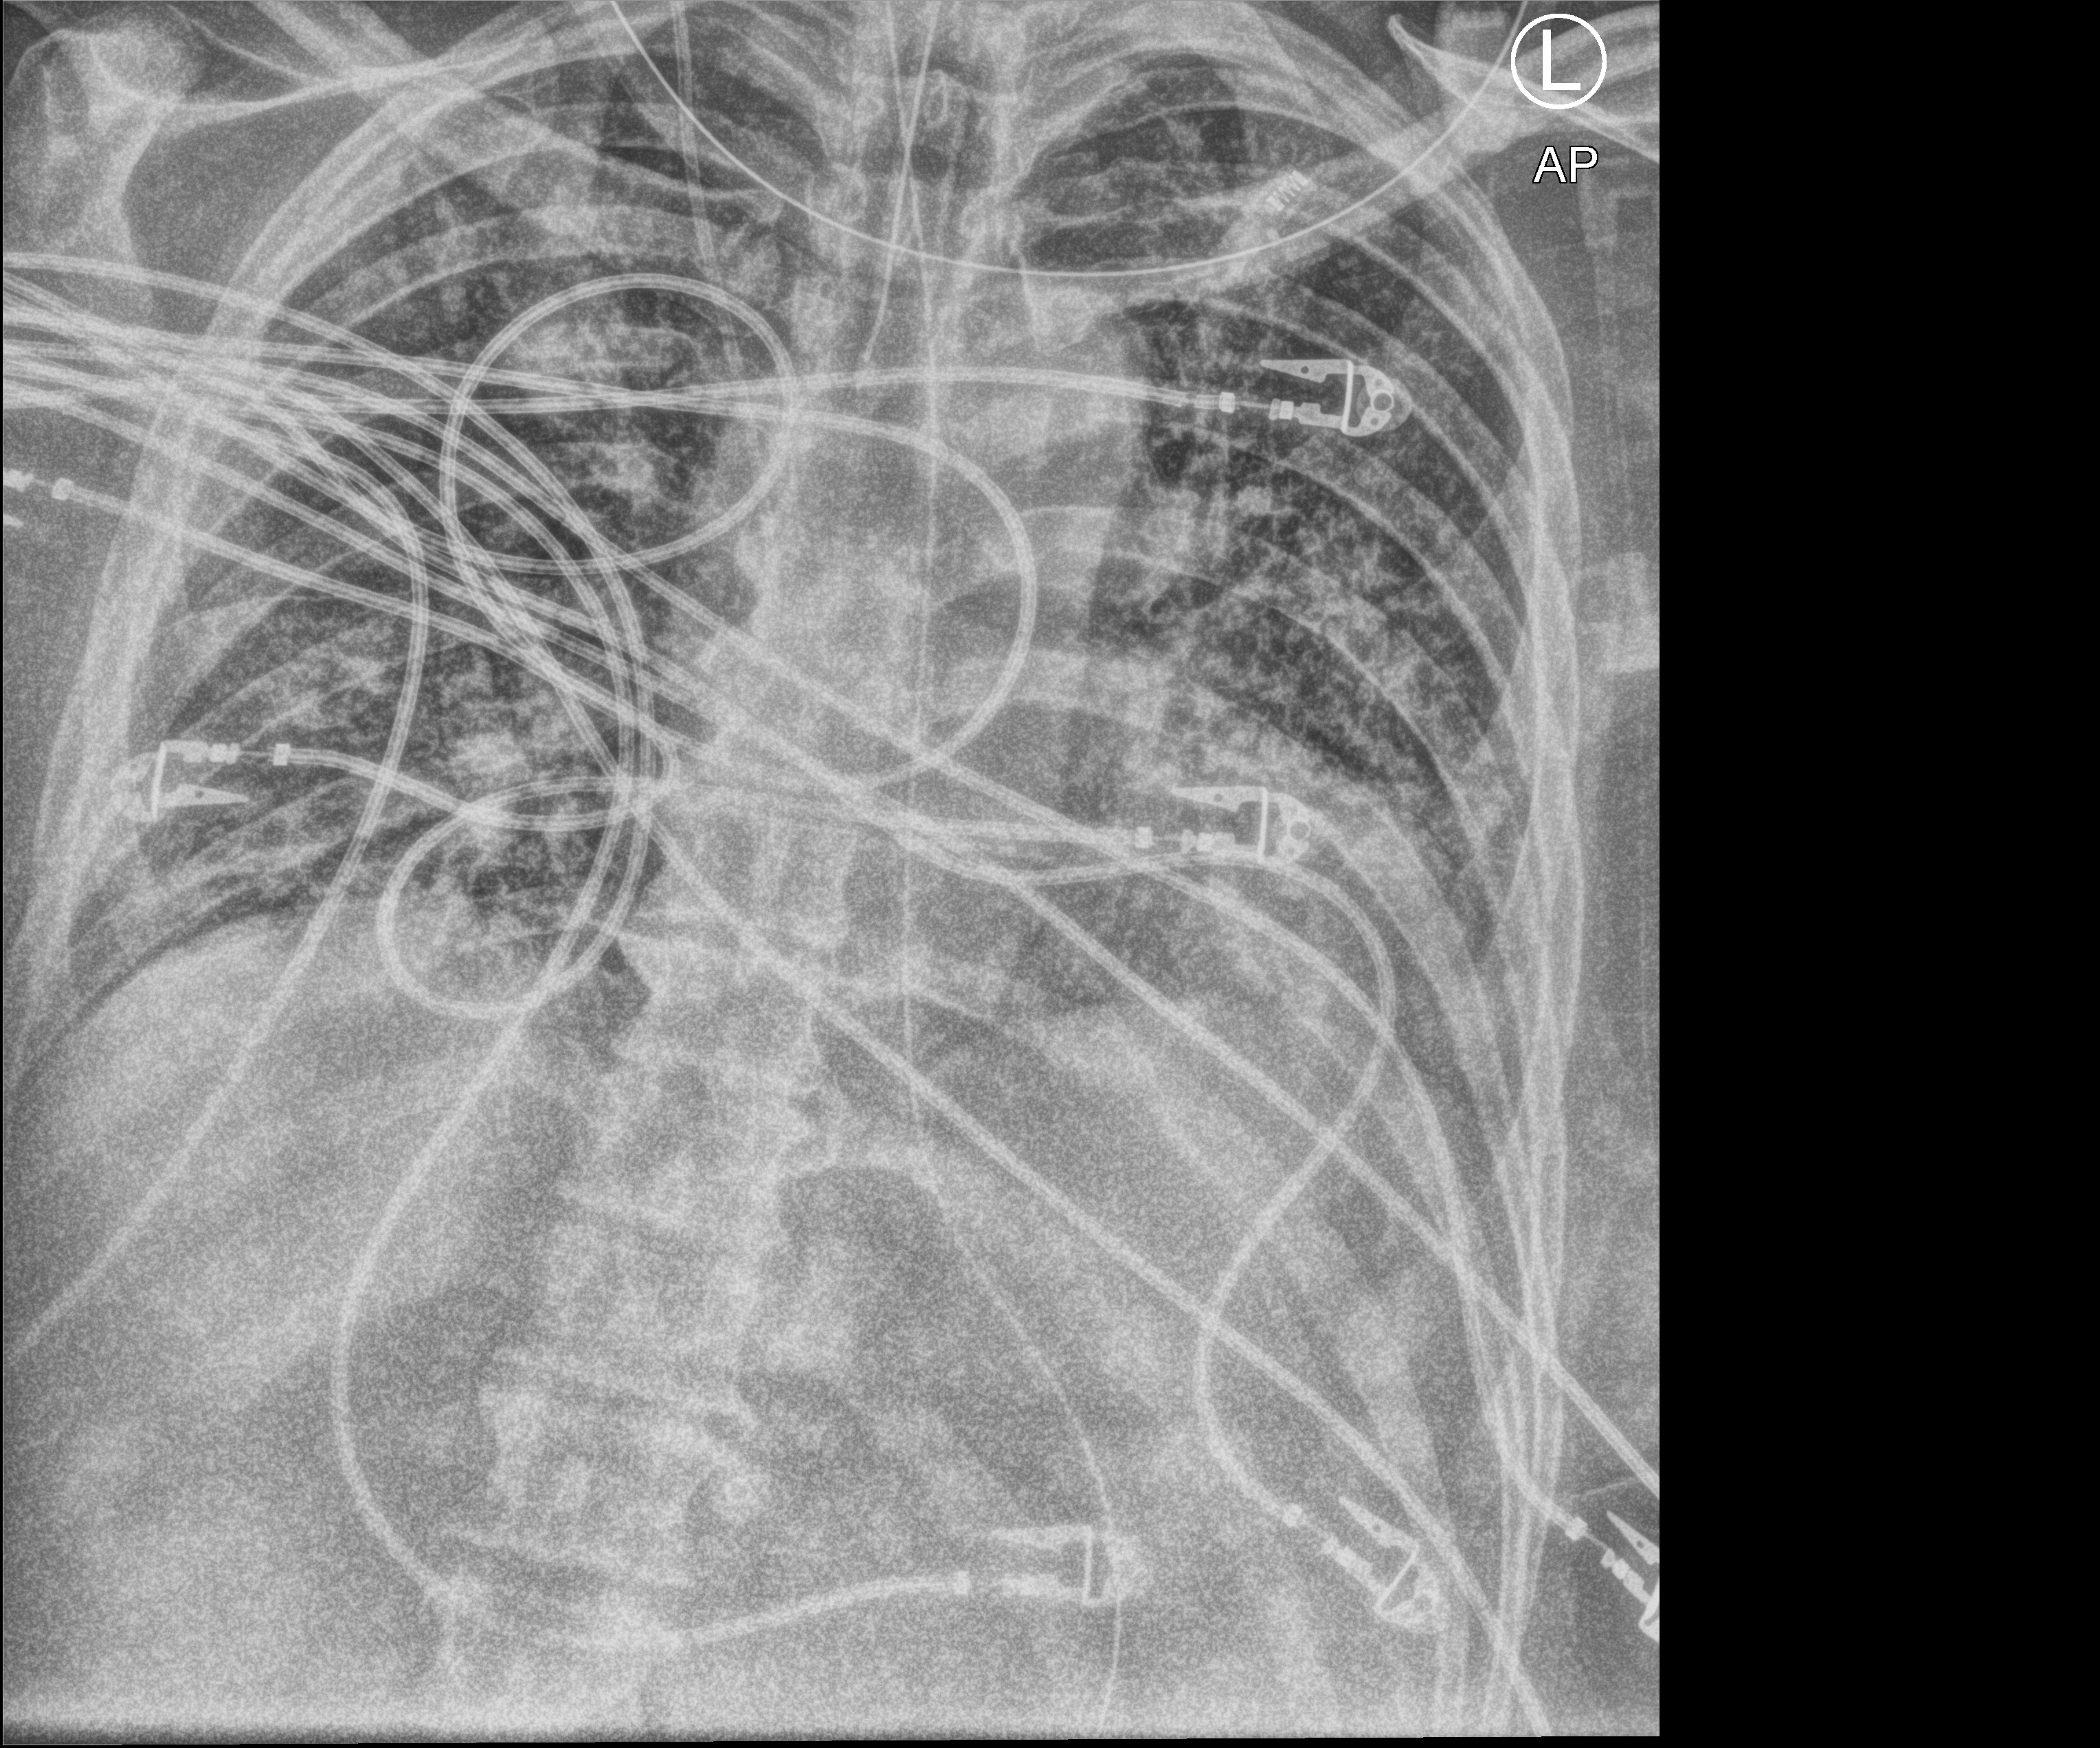
Portable chest radiograph, anteroposterior (AP) projection. Patient hospitalised with COVID-19; male, aged 60–74 years.
From the hospital-stay record, not from the radiograph (when in the stay this image was taken is not recorded): mechanically ventilated during this hospital stay: yes; COPD (admission record): no.